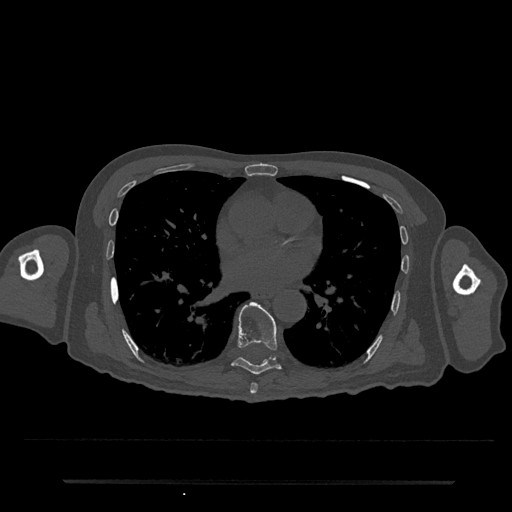
CT including the spine, one axial slice. Slice 421 of 797 in the series (ordered by position). Reconstruction kernel Br40s/3. Bone window (W 1800 / L 400 HU). 512 × 512 image matrix, field of view 427 × 427 mm. Patient: male, 74 years. From the clinical record (not read from this slice): primary cancer: prostate.
Annotated regions visible in this slice (semi-automatically segmented with operator editing):
- T7 vertebra: box from (x=250, y=383) to (x=258, y=394) px
- T8 vertebra: (x=231, y=302)–(x=281, y=375)